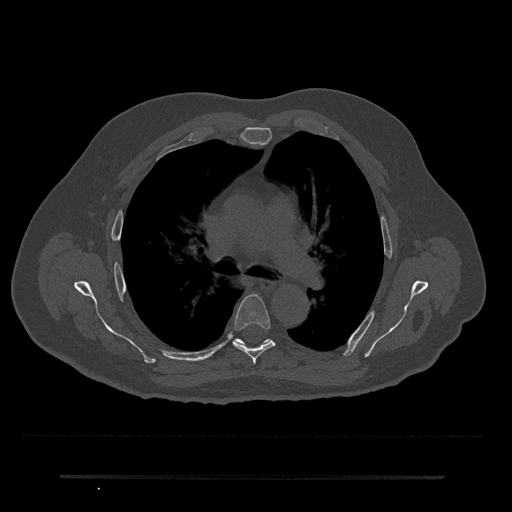
CT including the spine, one axial slice; slice 474 of 797 in the series (ordered by position); reconstruction kernel Br40s/3; bone window (W 1800 / L 400 HU); 0.5 mm slice thickness; 512 × 512 image matrix, field of view 437 × 437 mm. Male patient, age 69 years. From the clinical record (not read from this slice): primary cancer: prostate.
Structures marked on this image (semi-automatically segmented with operator editing):
- T5 vertebra: bounding box <233,294,275,364> (left, top, right, bottom; pixels)
- T6 vertebra: <238,340,240,342>